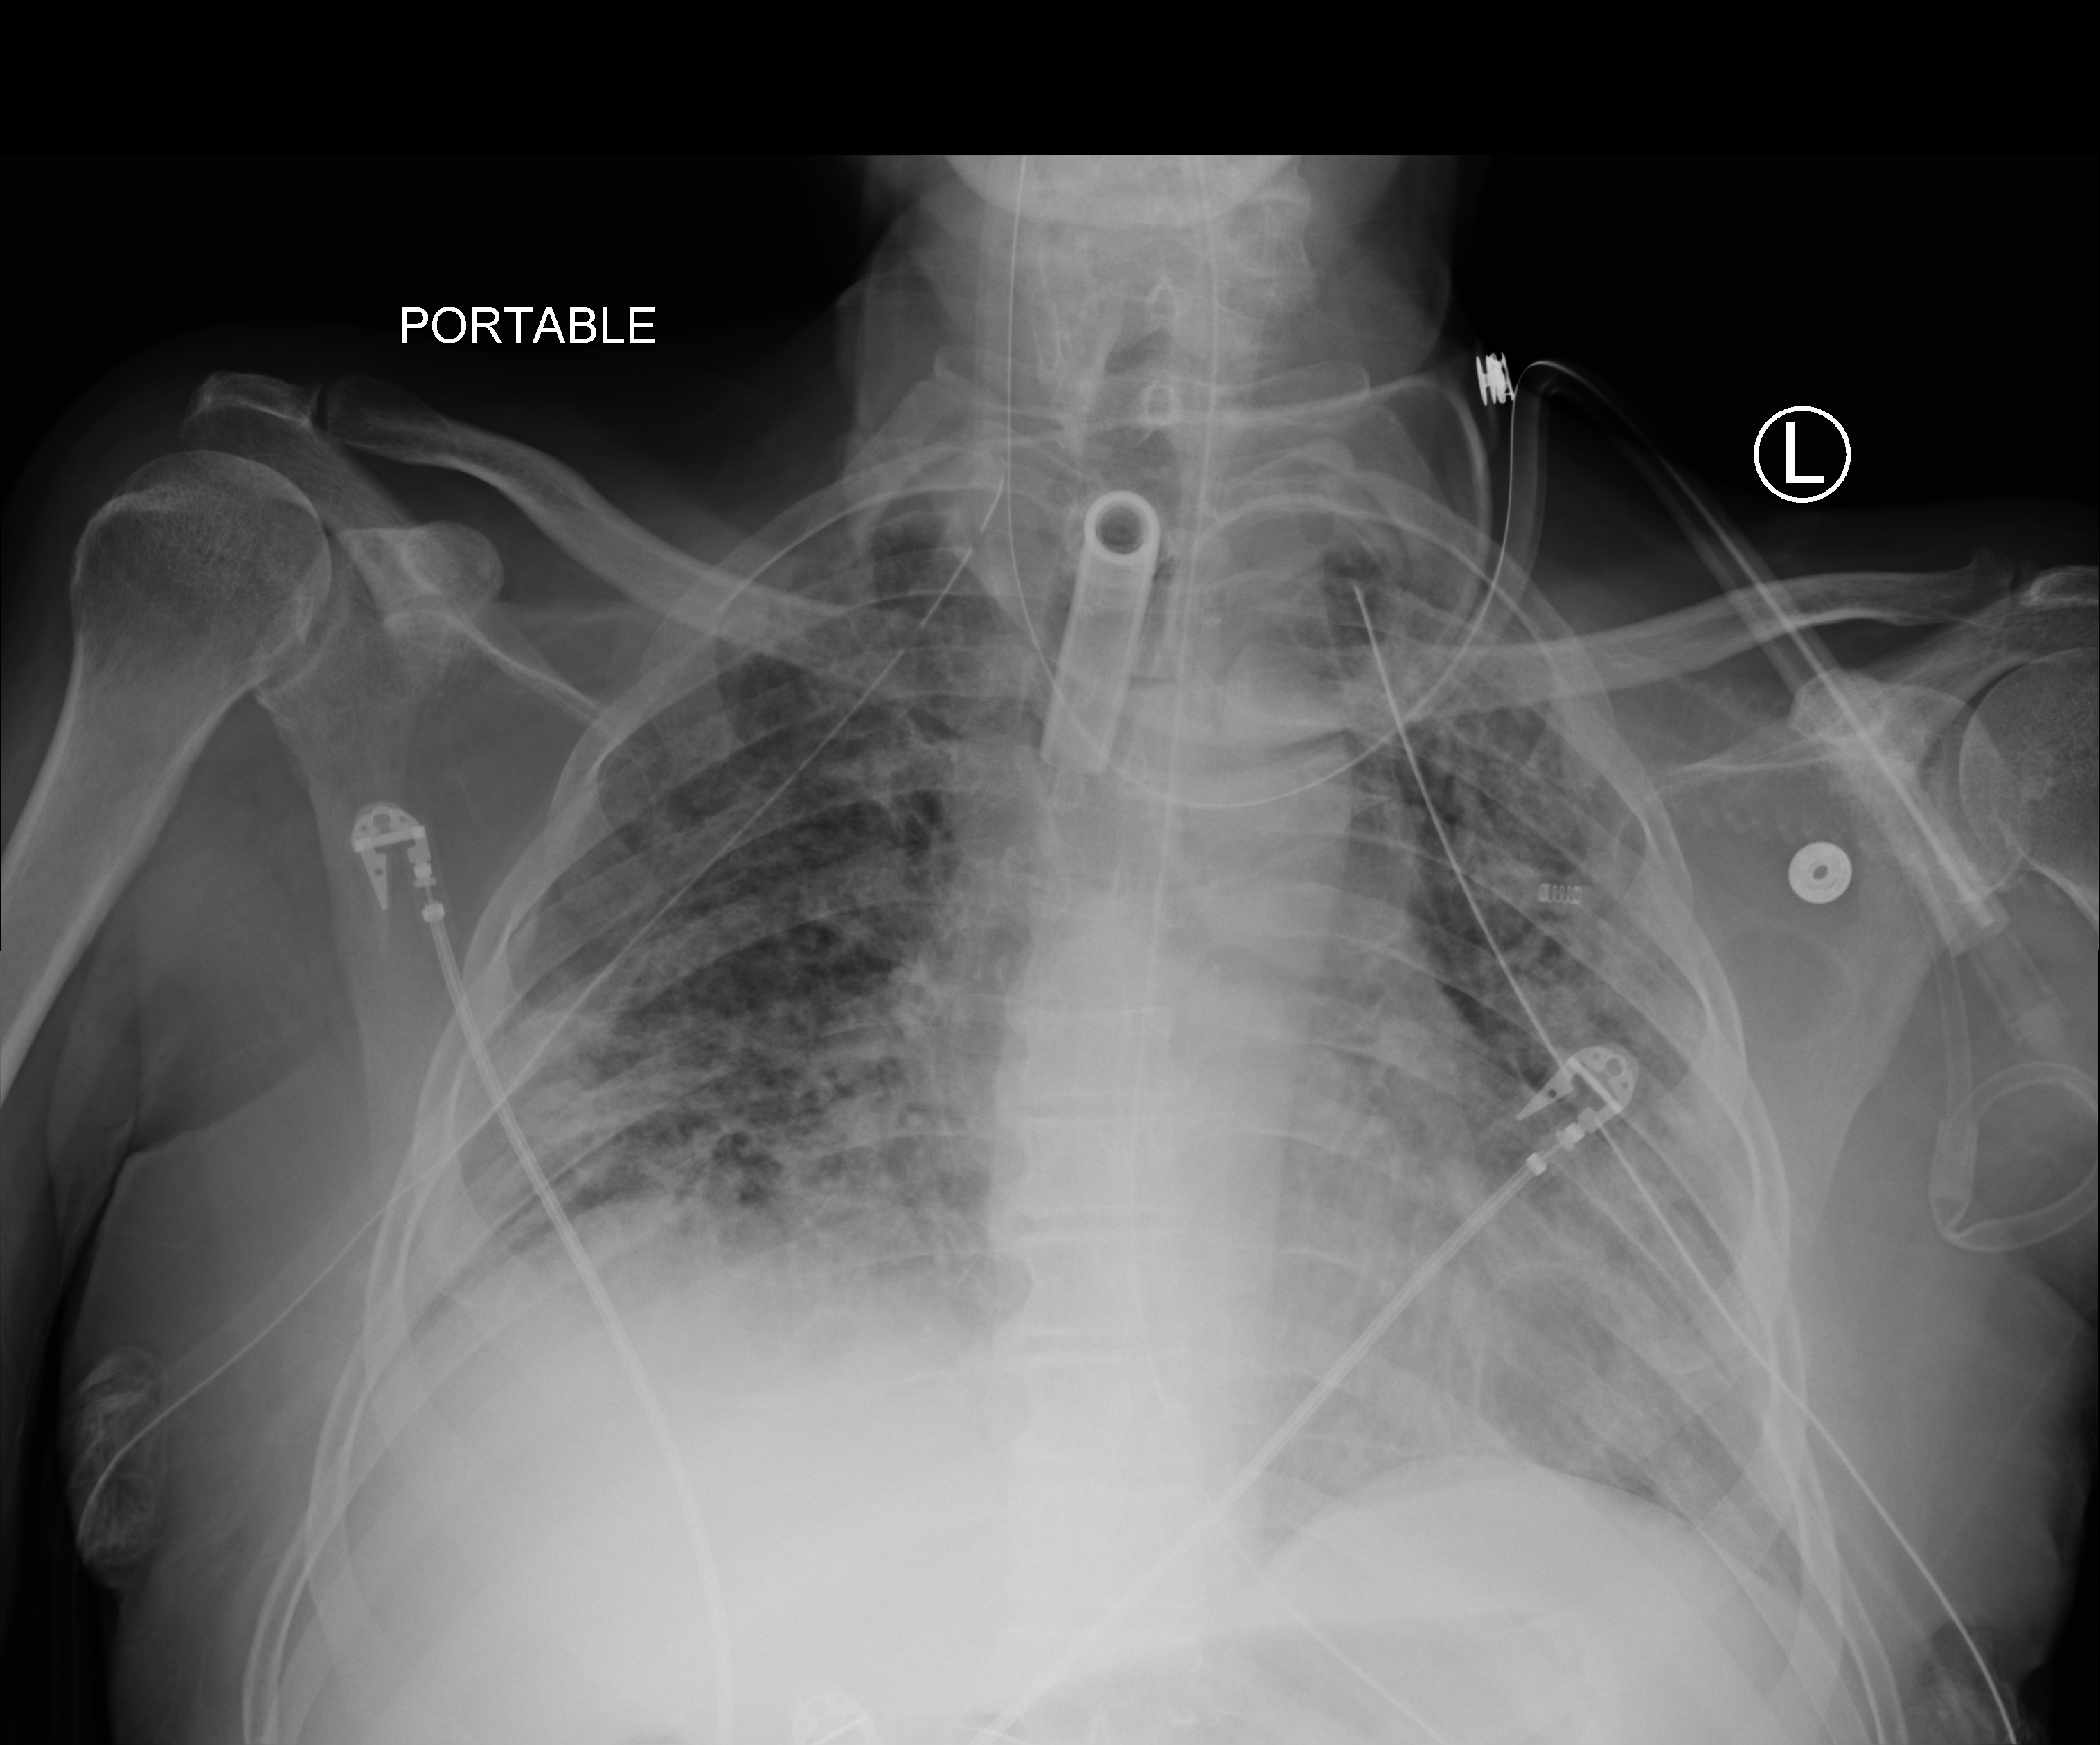
Chest X-ray (portable); anteroposterior (AP) projection. Male patient hospitalised with COVID-19, age 18–59 years.
Admission-level facts for this patient (not findings on this image; timing relative to this image not recorded): admitted to intensive care during this hospital stay: yes.